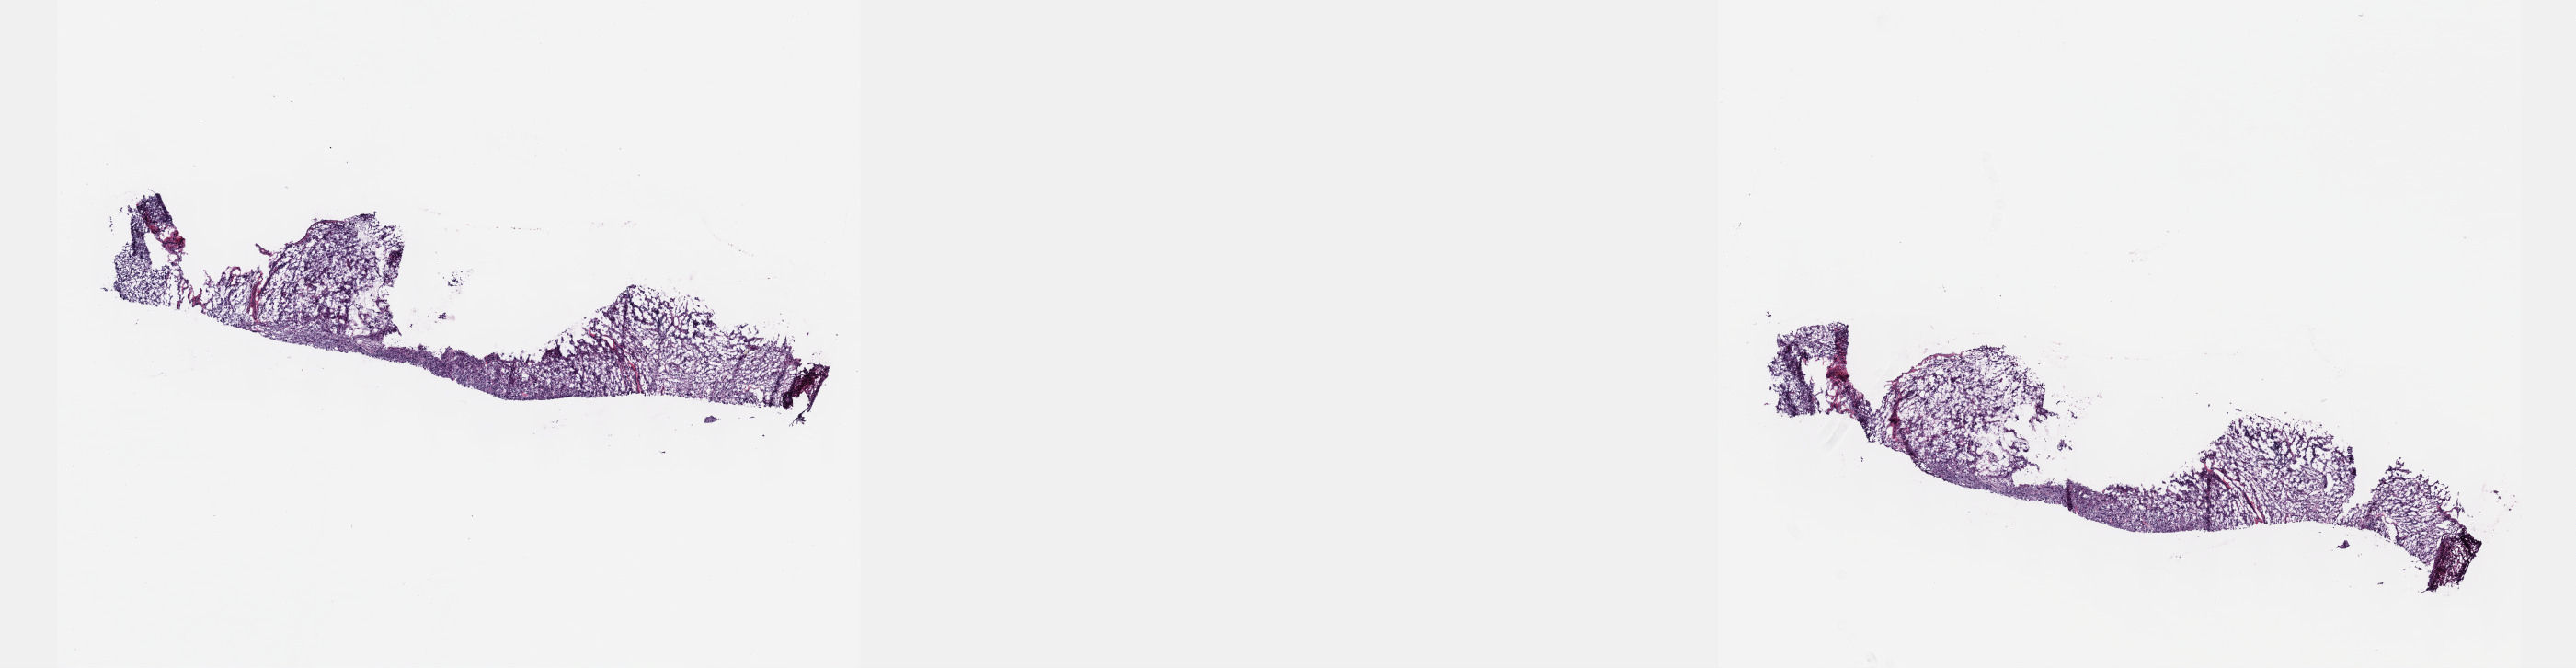
H&E-stained whole-slide image — whole scanned area (about 22.6 x 5.9 mm, from a 40x scan) shown as a low-resolution overview, frozen section from the top of the tissue portion, primary tumour sample from the connective, subcutaneous and other soft tissues. Patient: male, age at initial diagnosis 63 years. Pathologist review of this section (percent, as recorded): tumour cells 75%, tumour nuclei 75%, normal cells 0%, stromal cells 23%, necrosis 2%. Infiltration values recorded for this section: lymphocyte infiltration 3%, monocyte infiltration 1%, neutrophil infiltration 2%.
Diagnosis: Malignant fibrous histiocytoma (connective, subcutaneous and other soft tissues of lower limb and hip).